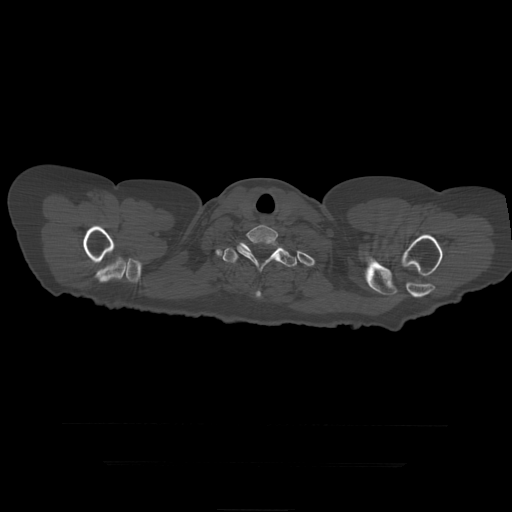
CT including the spine, one axial slice; slice 382 of 399 in the series (ordered by position); reconstruction kernel STANDARD; bone window (W 1800 / L 400 HU); 1.25 mm slice thickness; 512 × 512 image matrix, field of view 450 × 450 mm. Patient age 41 years. From the clinical record (not read from this slice): primary cancer: breast.
Annotated regions visible in this slice (semi-automatic segmentation, software-assisted and operator-edited):
- T1 vertebra: bounding box <237,225,279,272> (left, top, right, bottom; pixels)
- T2 vertebra: <223,240,297,297>